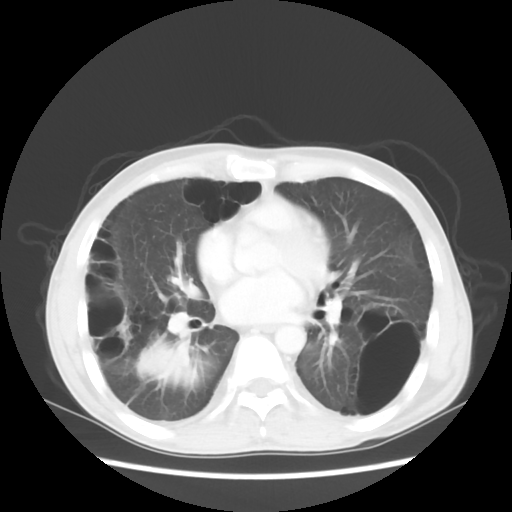
Chest CT, one axial slice; lung window (W 1500 / L -600 HU); 512 × 512 image matrix. Male patient, age 41 years. Case-level facts recorded for this patient, not image findings: clinical TNM (as recorded): T4 N0 M1a; histopathological grade: G3.
Annotated regions visible in this slice (bounding box drawn by a radiologist):
- lung tumour (recorded histology: large cell carcinoma): bounding box [x1, y1, x2, y2] px = [137, 333, 204, 391]